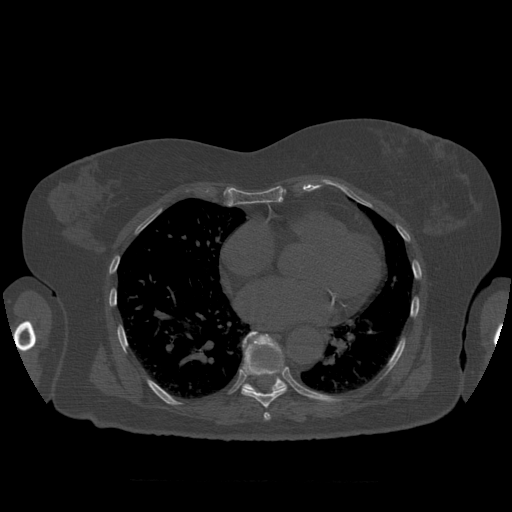
CT including the spine, one axial slice; slice 372 of 399 in the series (ordered by position); reconstruction kernel STANDARD; 120 kVp; bone window (W 1800 / L 400 HU); 1.25 mm slice thickness; 512 × 512 image matrix. Patient age 81 years. From the clinical record (not read from this slice): primary cancer: renal; vertebrae with lytic lesions (as recorded): L1.
Structures marked on this image (semi-automatic segmentation, software-assisted and operator-edited):
- T7 vertebra: bounding box (x1, y1, x2, y2) in pixels: (264, 412, 271, 420)
- T8 vertebra: (242, 334, 287, 408)
- T9 vertebra: (243, 332, 287, 393)